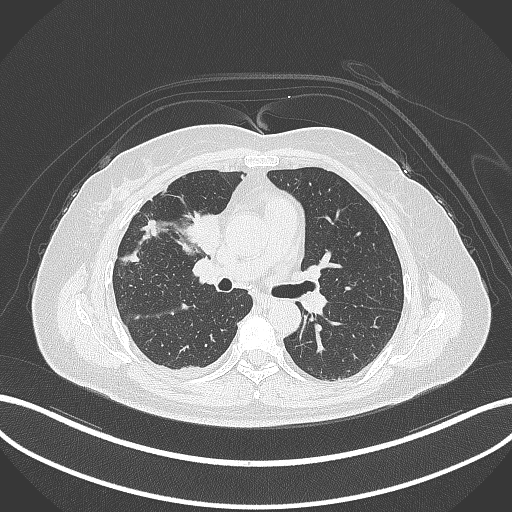
Chest CT, one axial slice; reconstruction kernel B70f; lung window (W 1500 / L -600 HU); 1 mm slice thickness; 512 × 512 image matrix. Female patient, age 52 years. Case-level facts recorded for this patient, not image findings: clinical TNM (as recorded): T3 N1 M1.
Structures marked on this image (bounding box drawn by a radiologist):
- lung tumour (recorded histology: adenocarcinoma): box from (x=176, y=208) to (x=223, y=254) px